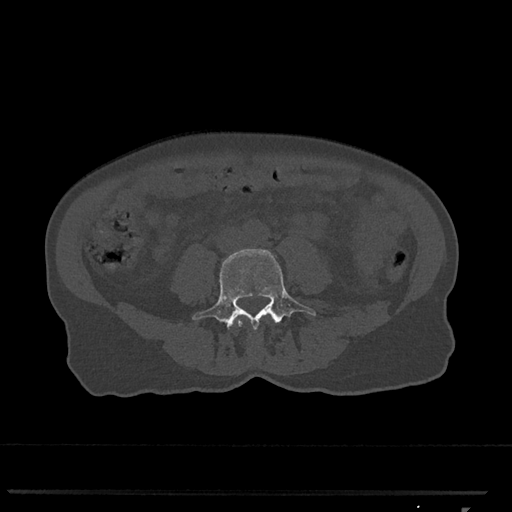
CT including the spine, one axial slice. Position 220 of 793 along the scan axis. 120 kVp. Bone window (W 1800 / L 400 HU). 512 × 512 image matrix, field of view 380 × 380 mm. Patient: female, 62 years. From the clinical record (not read from this slice): primary cancer: renal.
Structures marked on this image (semi-automatically segmented with operator editing):
- L3 vertebra: bounding box (x1, y1, x2, y2) in pixels: (235, 319, 242, 325)
- L4 vertebra: (192, 248, 316, 330)